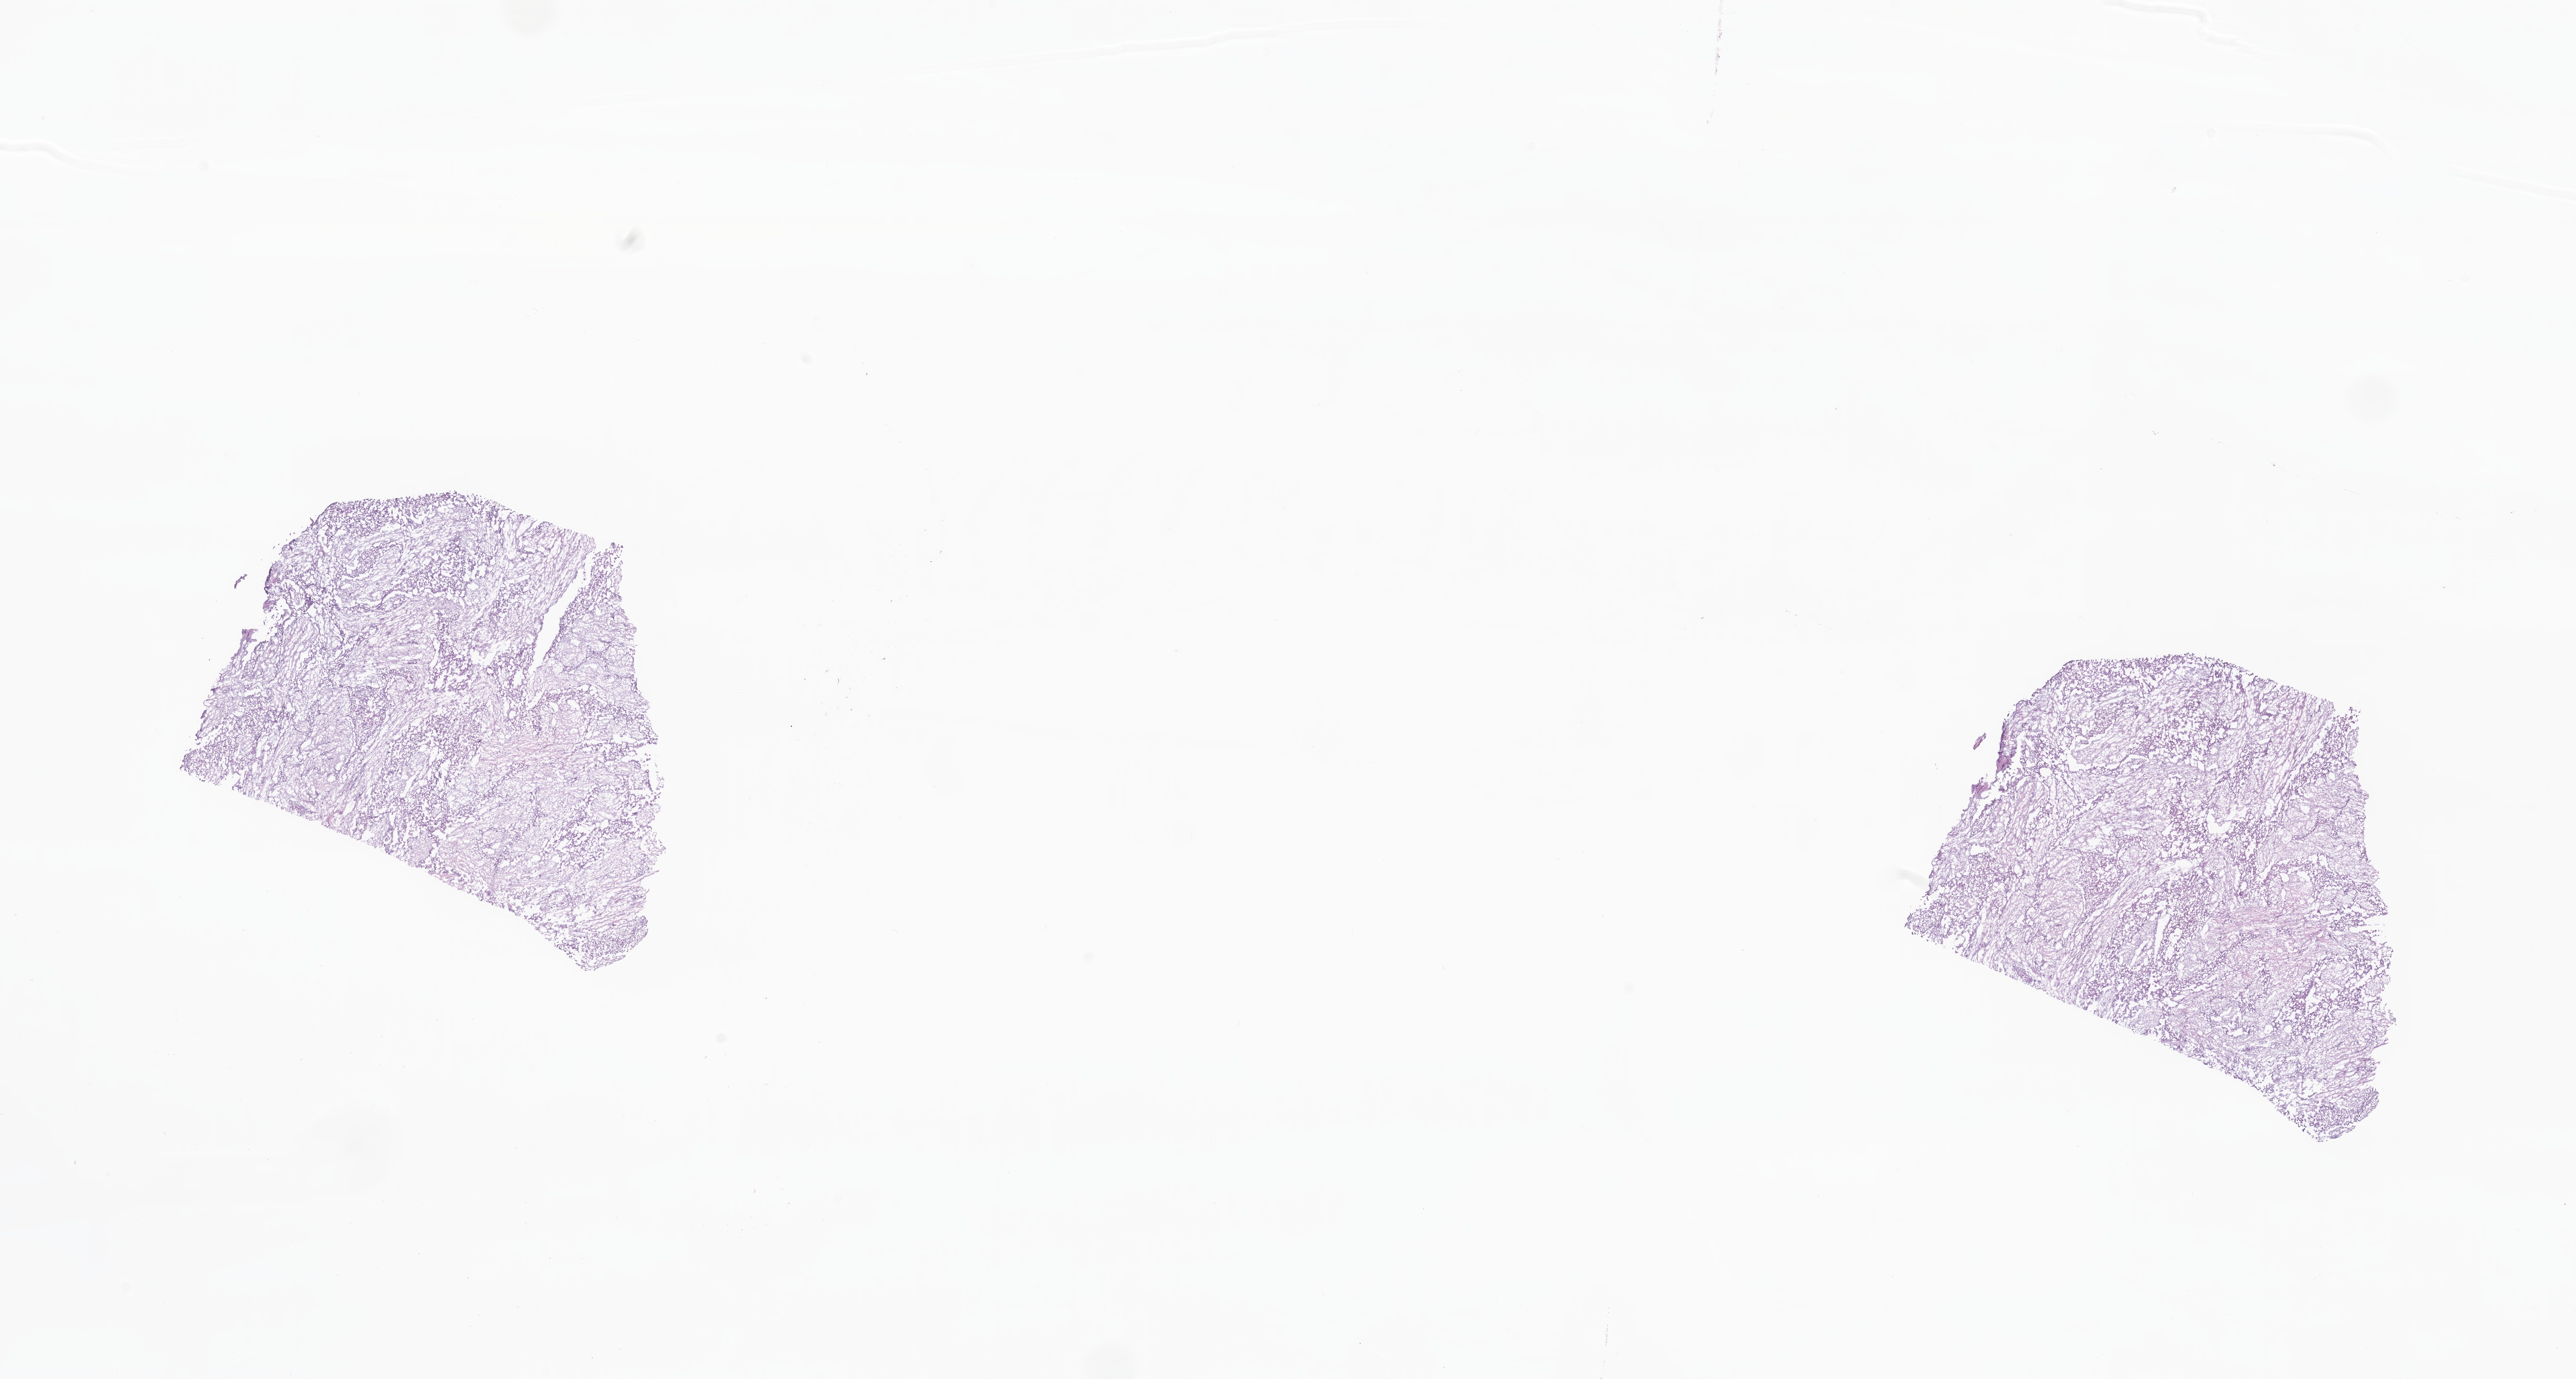
H&E whole-slide image — low-resolution overview of the scanned area, about 26.2 x 14.0 mm. Frozen section. Primary tumor. Site: tail of pancreas. Male, age 64 years at initial diagnosis. Pathologist review of this section (percent, as recorded): tumor cells 40%, tumor nuclei 50%, stromal cells 60%, necrosis 0%, normal cells 0%. Infiltration values recorded for this section: lymphocyte infiltration 0%, monocyte infiltration 0%, neutrophil infiltration 0%.
- section: bottom of the tissue portion
- diagnosis: Mixed adenoneuroendocrine carcinoma